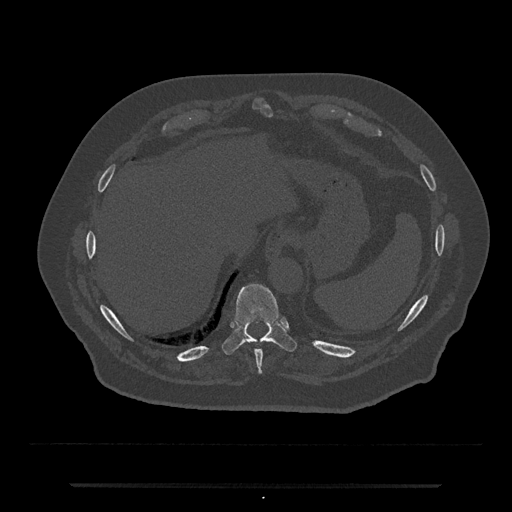
CT including the spine, one axial slice; slice 718 of 797 in the series (ordered by position); reconstruction kernel Br40s/3; 120 kVp; bone window (W 1800 / L 400 HU); 512 × 512 image matrix, field of view 434 × 434 mm. Male patient, age 80 years. Case-level facts recorded for this patient, not image findings: primary cancer: prostate.
Structures marked on this image (semi-automatic segmentation, software-assisted and operator-edited):
- T10 vertebra: bounding box <222,284,296,355> (left, top, right, bottom; pixels)
- T9 vertebra: <255,349,263,374>